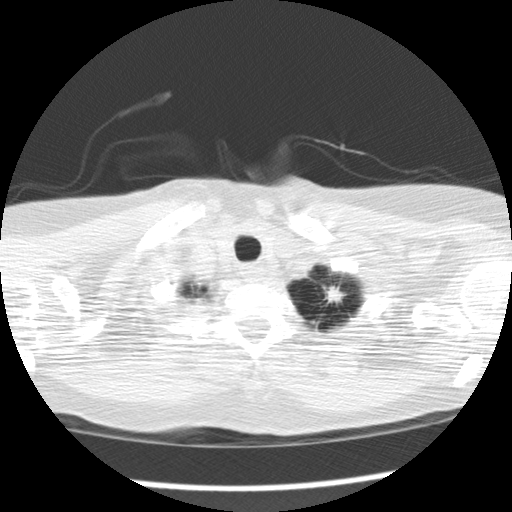
Chest CT (low-dose screening protocol), one axial image, second screening round (one year after baseline), lung window (W 1500 / L -600 HU), 2.5 mm slice thickness, 120 kVp, slice 151 of 159 in the series, 512 × 512 image matrix. Female, age 69 years at enrolment. Former smoker at enrolment.
Lesion marked by an expert reader, box from (x=309, y=274) to (x=356, y=318) px. The screening reader recorded 2 non-calcified nodules or masses ≥4 mm on this exam; which of them this box marks is not recorded. Official screen result: positive, change unspecified: nodule(s) >= 4 mm or enlarging nodule(s), mass(es), or other non-specific abnormalities suspicious for lung cancer.